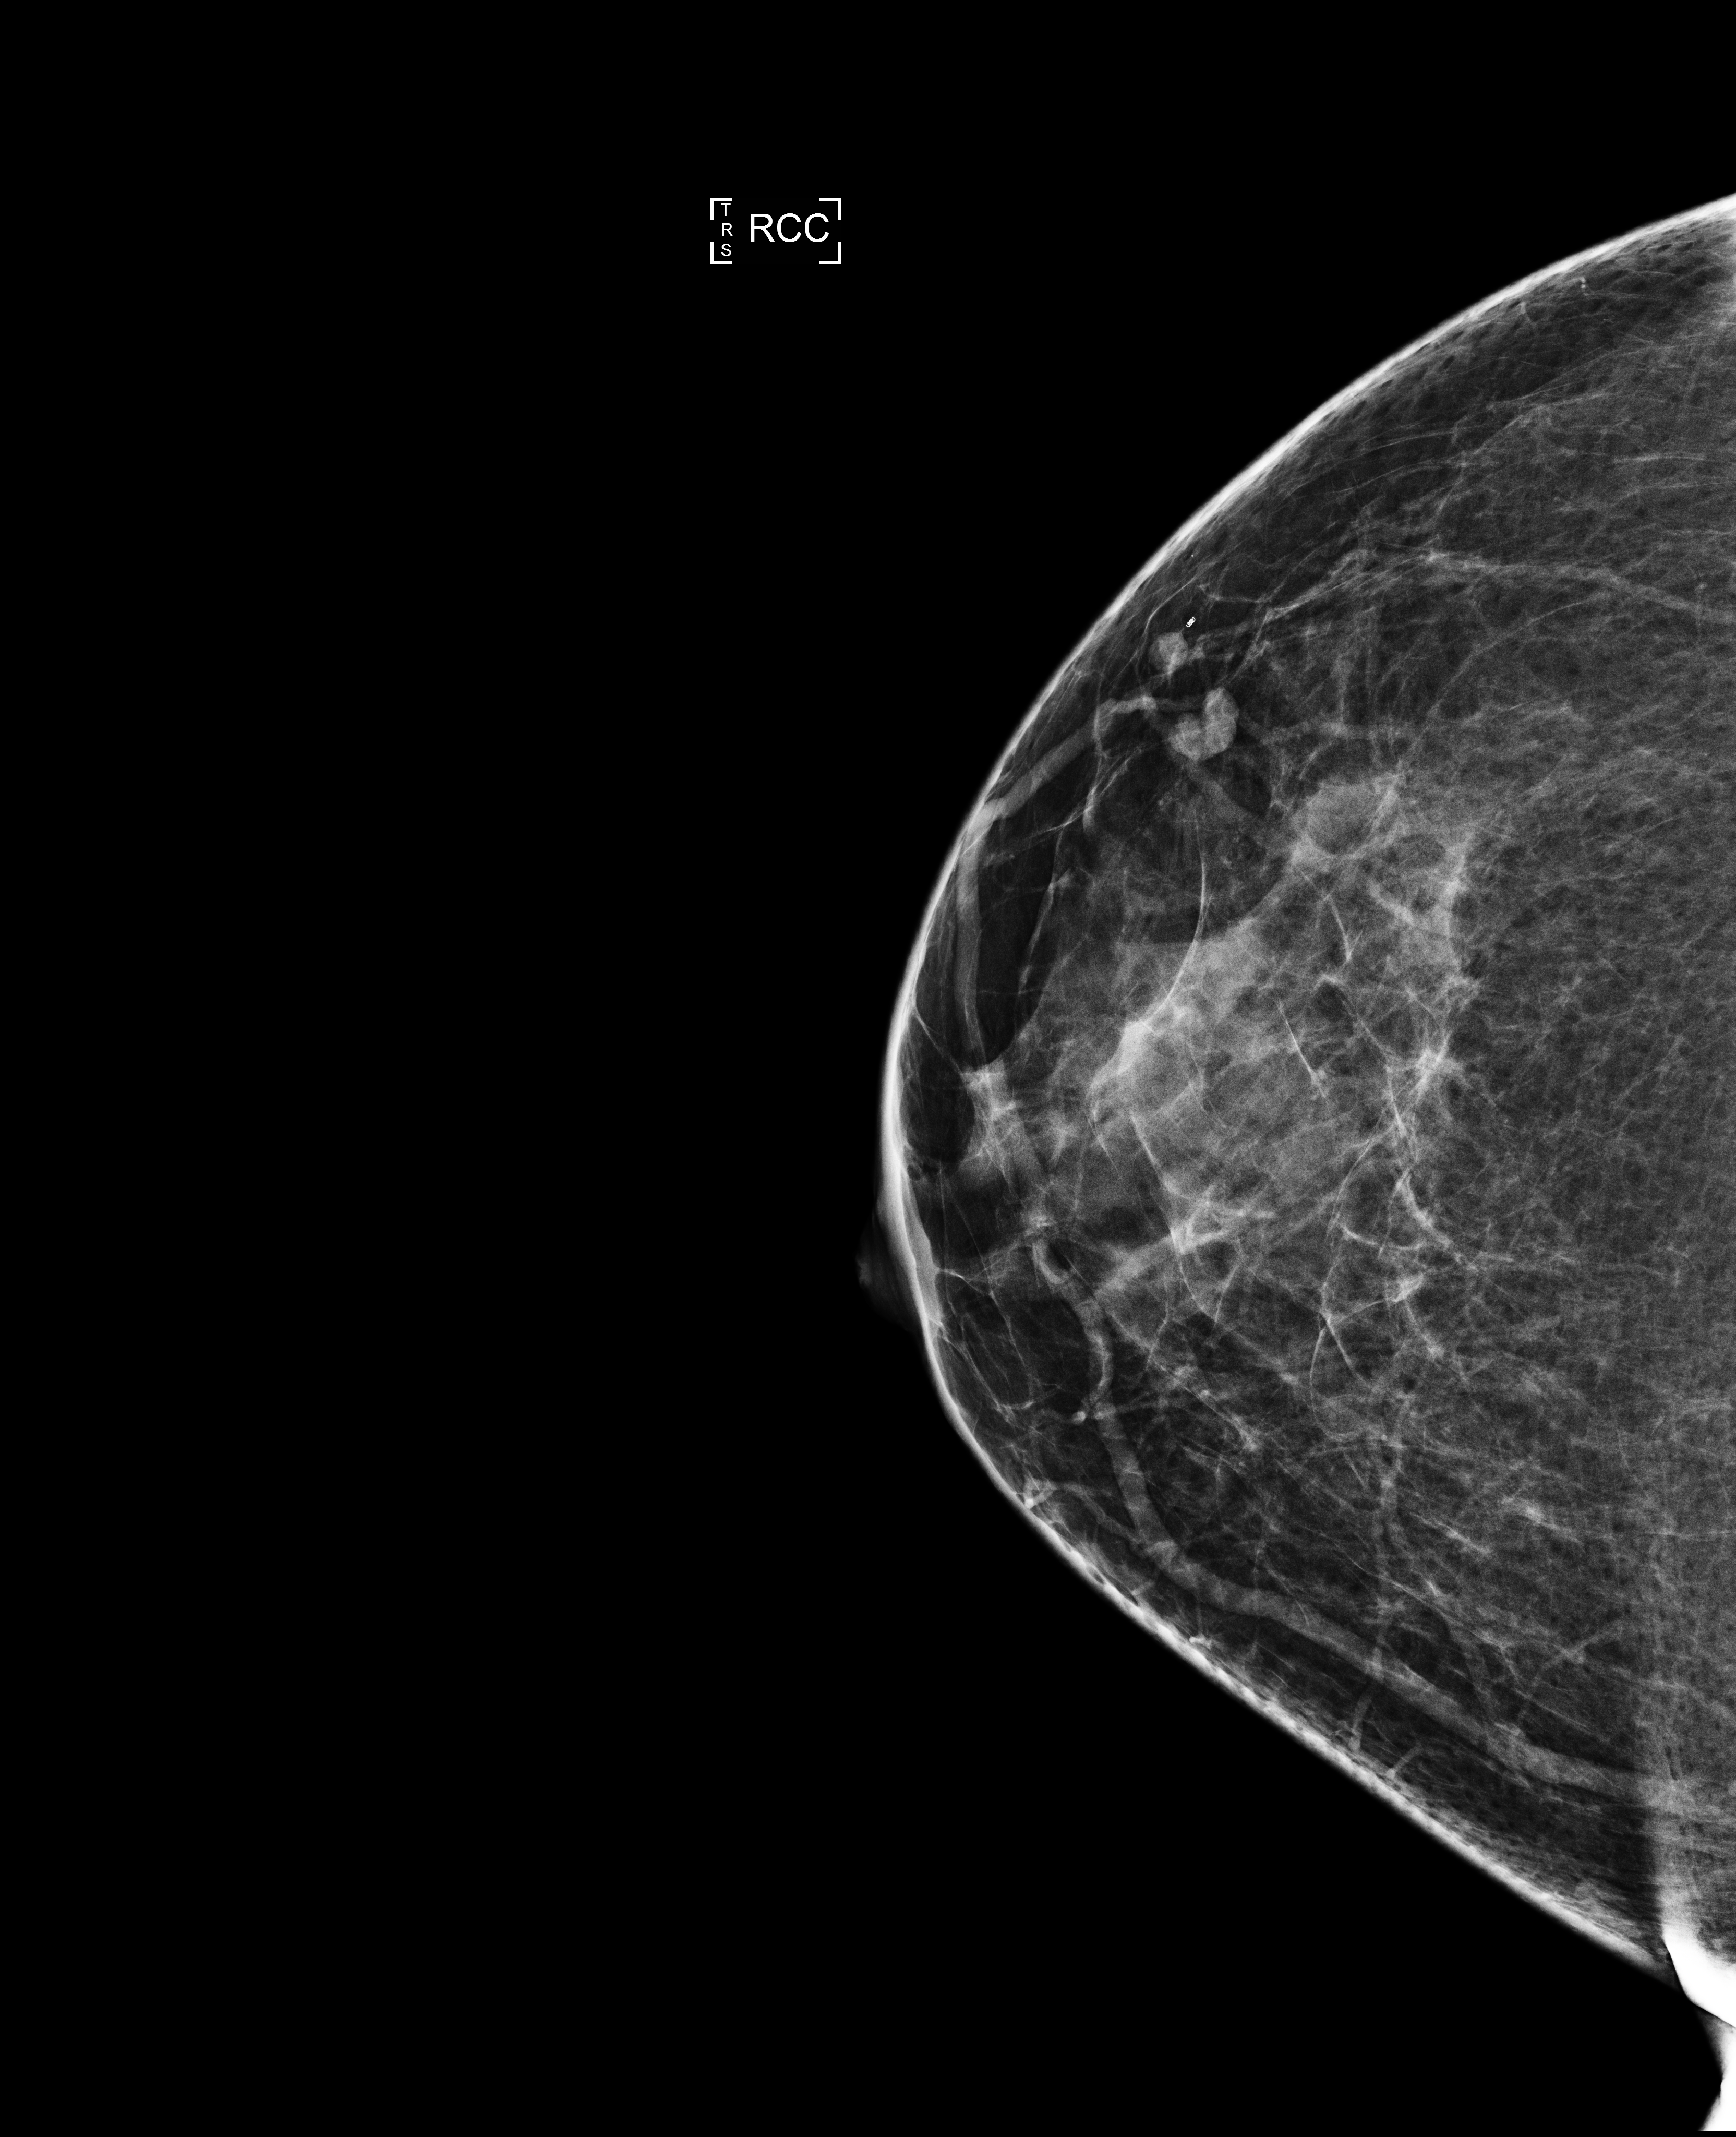
Screening examination. Patient: female, 47 years.
Image type: full-field digital mammogram. Breast: right. Projection: craniocaudal (CC) view.